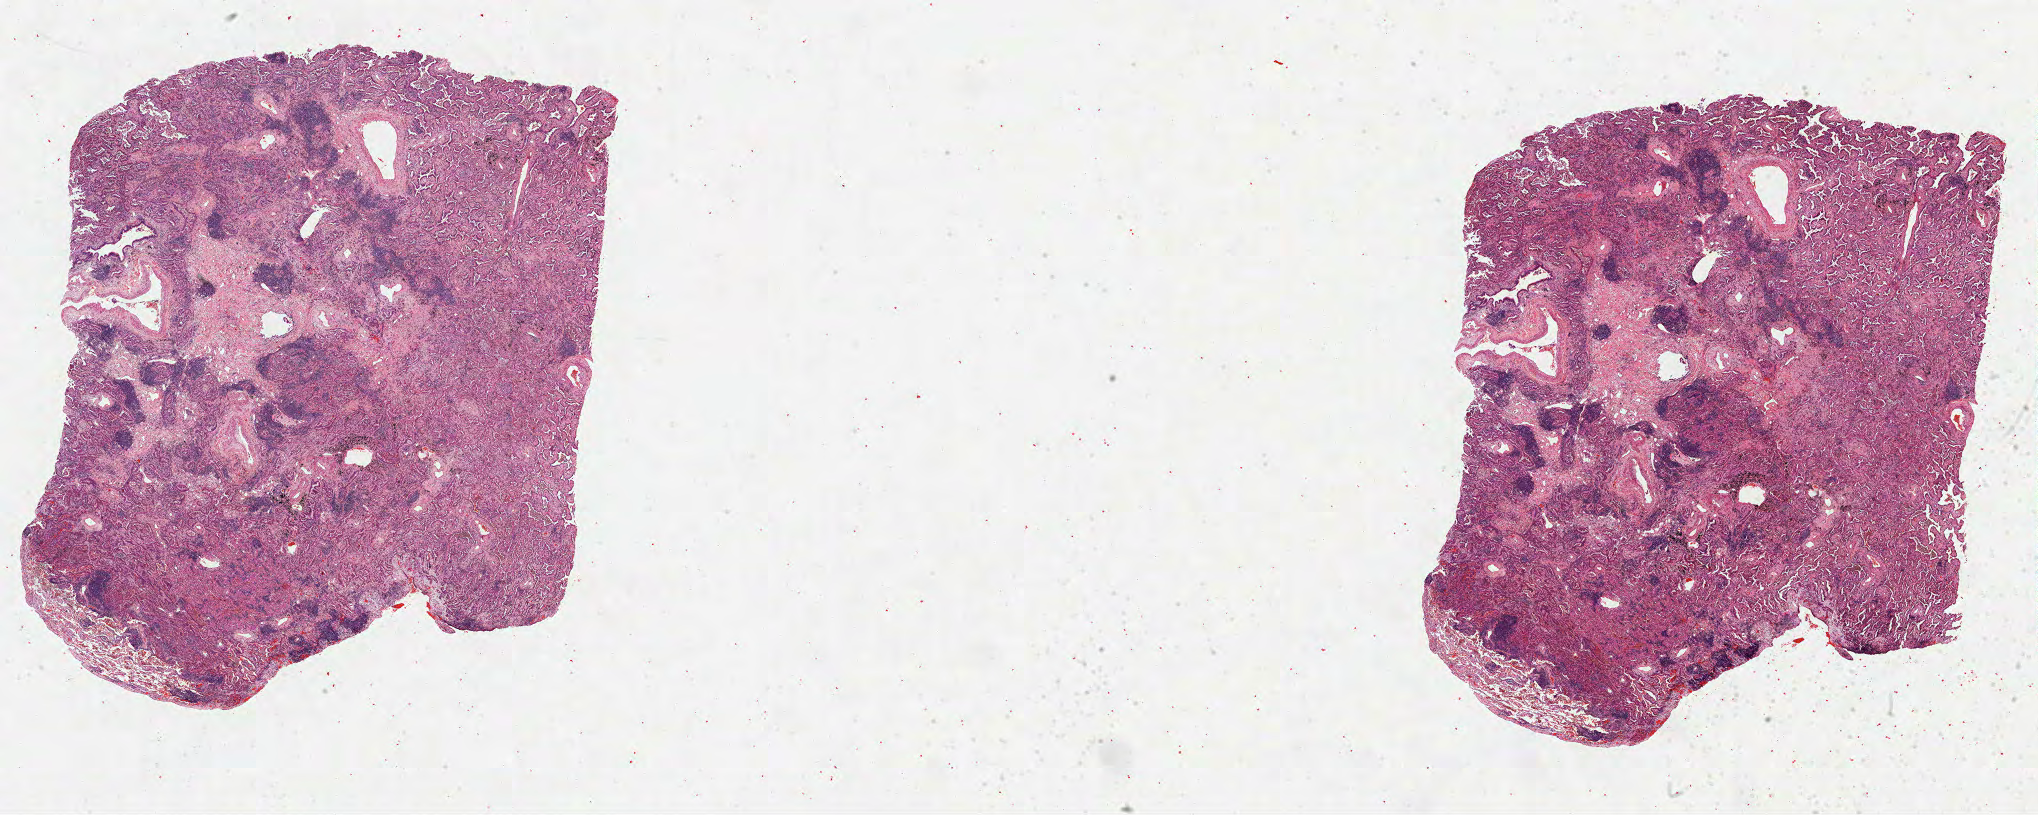
H&E-stained whole-slide image, whole scanned area (about 32.9 x 13.1 mm, slide scanned at 40x) shown as a low-resolution overview; formalin-fixed paraffin-embedded (FFPE) diagnostic section; primary tumour sample from the lung. Female, age 73 years at initial diagnosis.
- AJCC pathologic stage: IIA
- histologic diagnosis: Adenocarcinoma, NOS (upper lobe, lung)